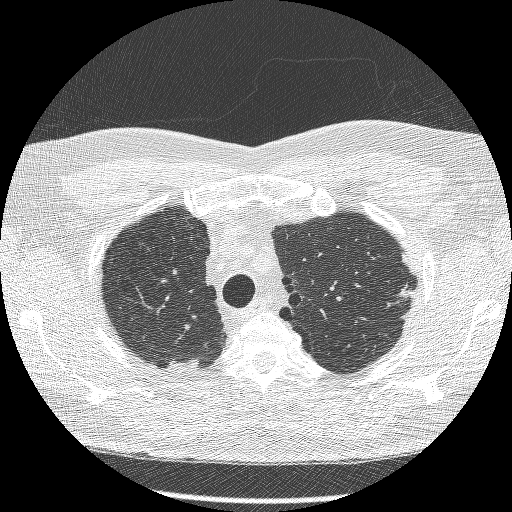
Chest CT (low-dose screening protocol), one axial image; second screening round (one year after baseline); lung window (W 1500 / L -600 HU); 1.25 mm slice thickness; slice 224 of 269 in the series; 512 × 512 image matrix. Male, age 66 years at enrolment. Current smoker at enrolment.
• Expert reader's lesion annotation, box from (x=382, y=261) to (x=428, y=315) px.
• The exam's reader record, not a measurement of the box and not confirmed to be the same lesion: non-calcified nodule or mass ≥4 mm, right lower lobe, 40 × 19 mm, spiculated (stellate) margins, soft tissue attenuation, pre-existing on the prior screen: yes; interval growth: no.
• Note: the box lies in the patient's left hemithorax on this image, whereas the reader's record names the right lung; they may be different findings.
• Official screen result: negative screen, minor abnormalities not suspicious for lung cancer.